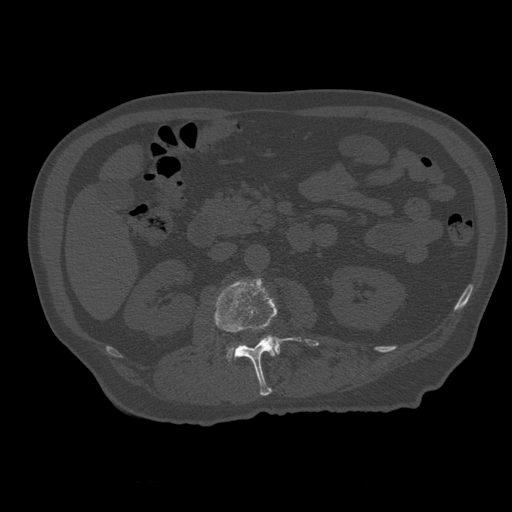
CT including the spine, one axial slice; slice 210 of 399 in the series (ordered by position); reconstruction kernel STANDARD; 120 kVp; bone window (W 1800 / L 400 HU); 512 × 512 image matrix, field of view 407 × 407 mm. Patient age 73 years. From the clinical record (not read from this slice): primary cancer: prostate; vertebrae with lytic lesions (as recorded): L2.
Outlined on this slice (semi-automatic segmentation, software-assisted and operator-edited):
- L2 vertebra: box from (x=214, y=279) to (x=302, y=396) px
- L3 vertebra: (x=227, y=337)–(x=281, y=360)